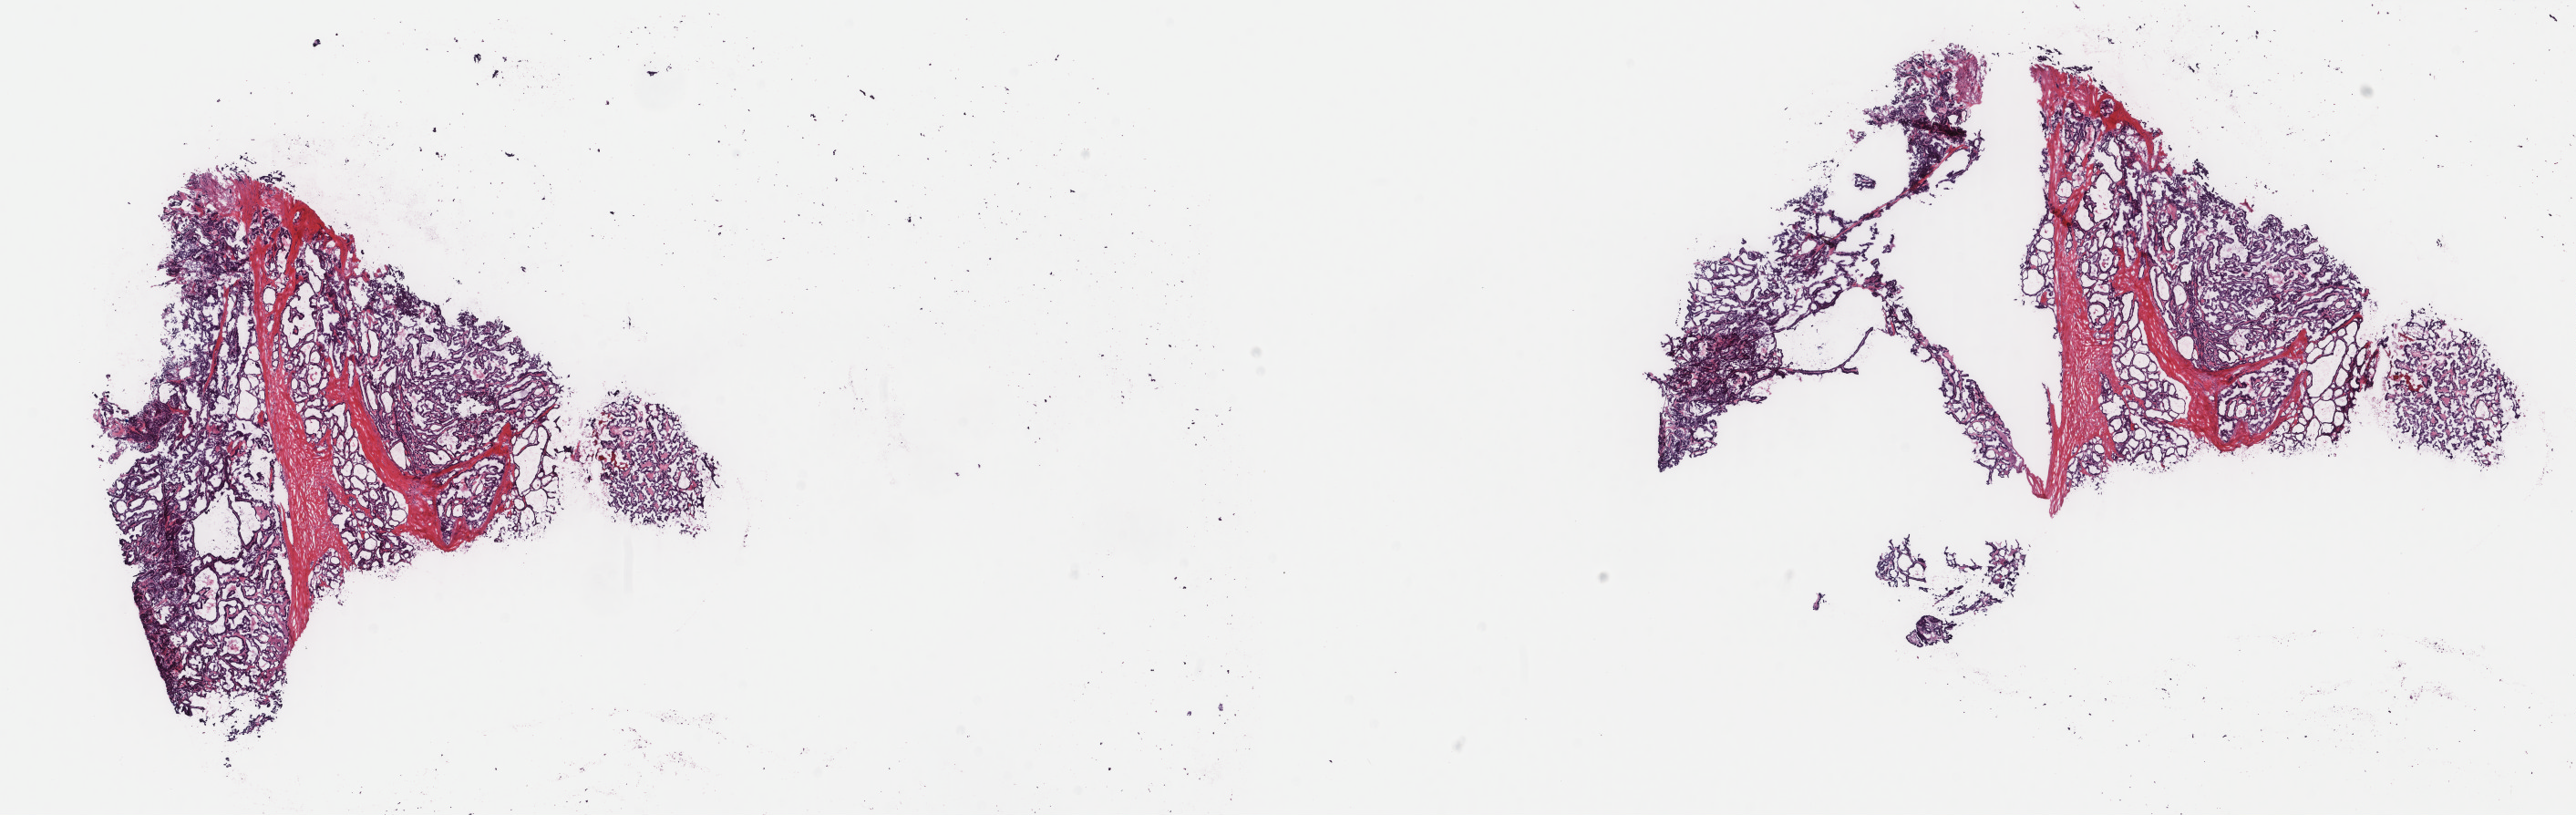
Digitized H&E-stained tissue section (whole slide) — low-resolution overview of the scanned area, about 22.4 x 7.1 mm (from a 40x scan). Frozen section from the top of the tissue portion. Sample: primary tumour, thyroid. Male patient; age at initial diagnosis 26 years.
Pathologic diagnosis: Papillary adenocarcinoma, NOS (thyroid gland).